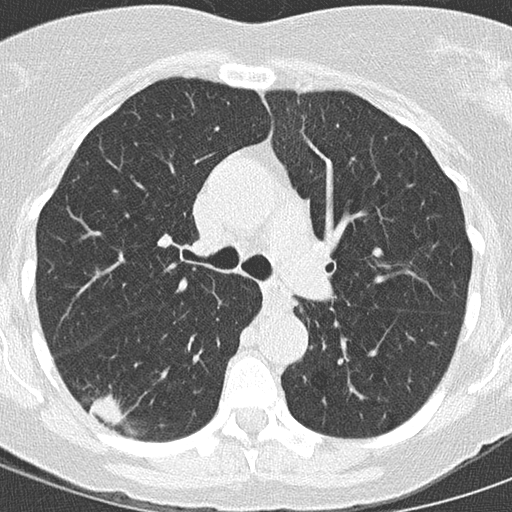
Axial slice from a low-dose chest CT screening exam; baseline annual screen; lung window (W 1500 / L -600 HU); 2 mm slice thickness; lung (sharp) reconstruction kernel (B50f); slice 55 of 146 in the series; 512 × 512 image matrix. Female, age 59 years at enrolment. Former smoker at enrolment.
Lesion marked by an expert reader, bounding box (x1, y1, x2, y2) in pixels: (72, 384, 147, 441). Reader record for this screening exam (exam-level; its link to the box is not recorded): non-calcified nodule or mass ≥4 mm, right lower lobe, 24 × 15 mm, spiculated (stellate) margins, soft tissue attenuation. Official screen result: positive, change unspecified: nodule(s) >= 4 mm or enlarging nodule(s), mass(es), or other non-specific abnormalities suspicious for lung cancer.